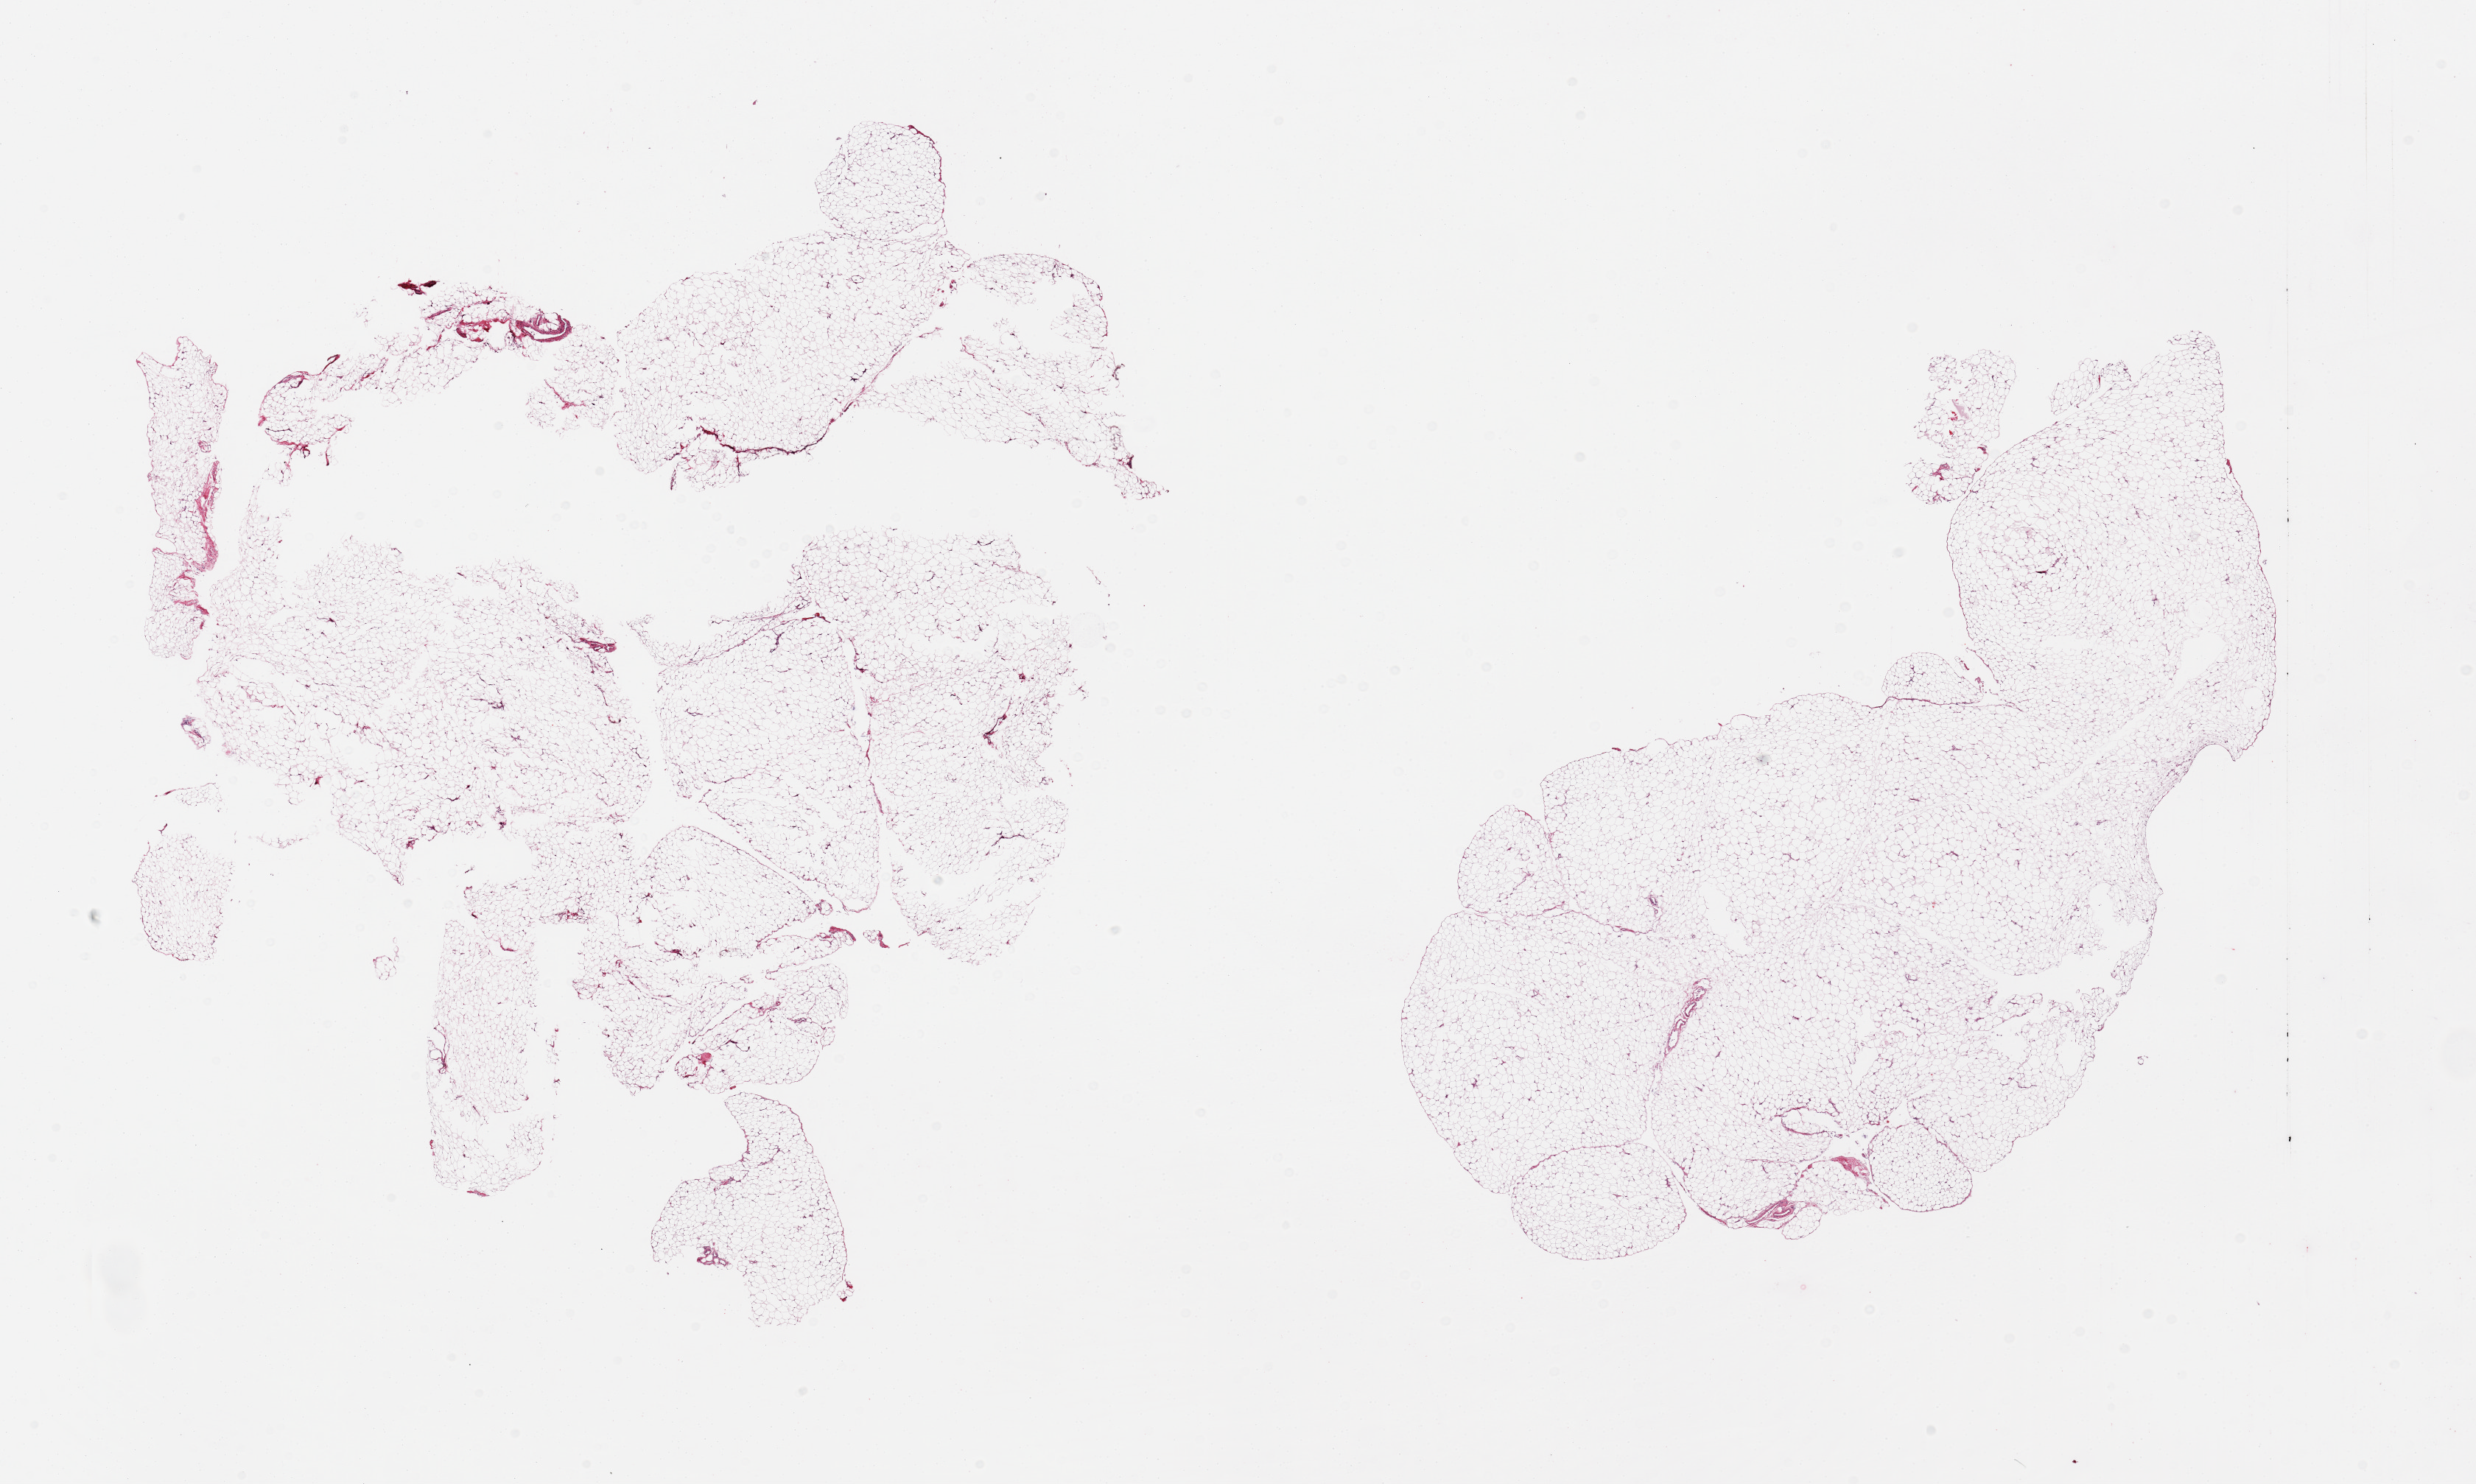
Digitized hematoxylin and eosin (H&E)-stained section — a low-resolution overview of the entire scanned area, about 26.6 x 15.9 mm; PAXgene-fixed paraffin-embedded (PFPE) section; sampled site (target tissue): omentum; donor tissue sample. Donor sex: female.
* reviewer comment on this tissue sample: 2 pieces no significant fascia/vascular elements